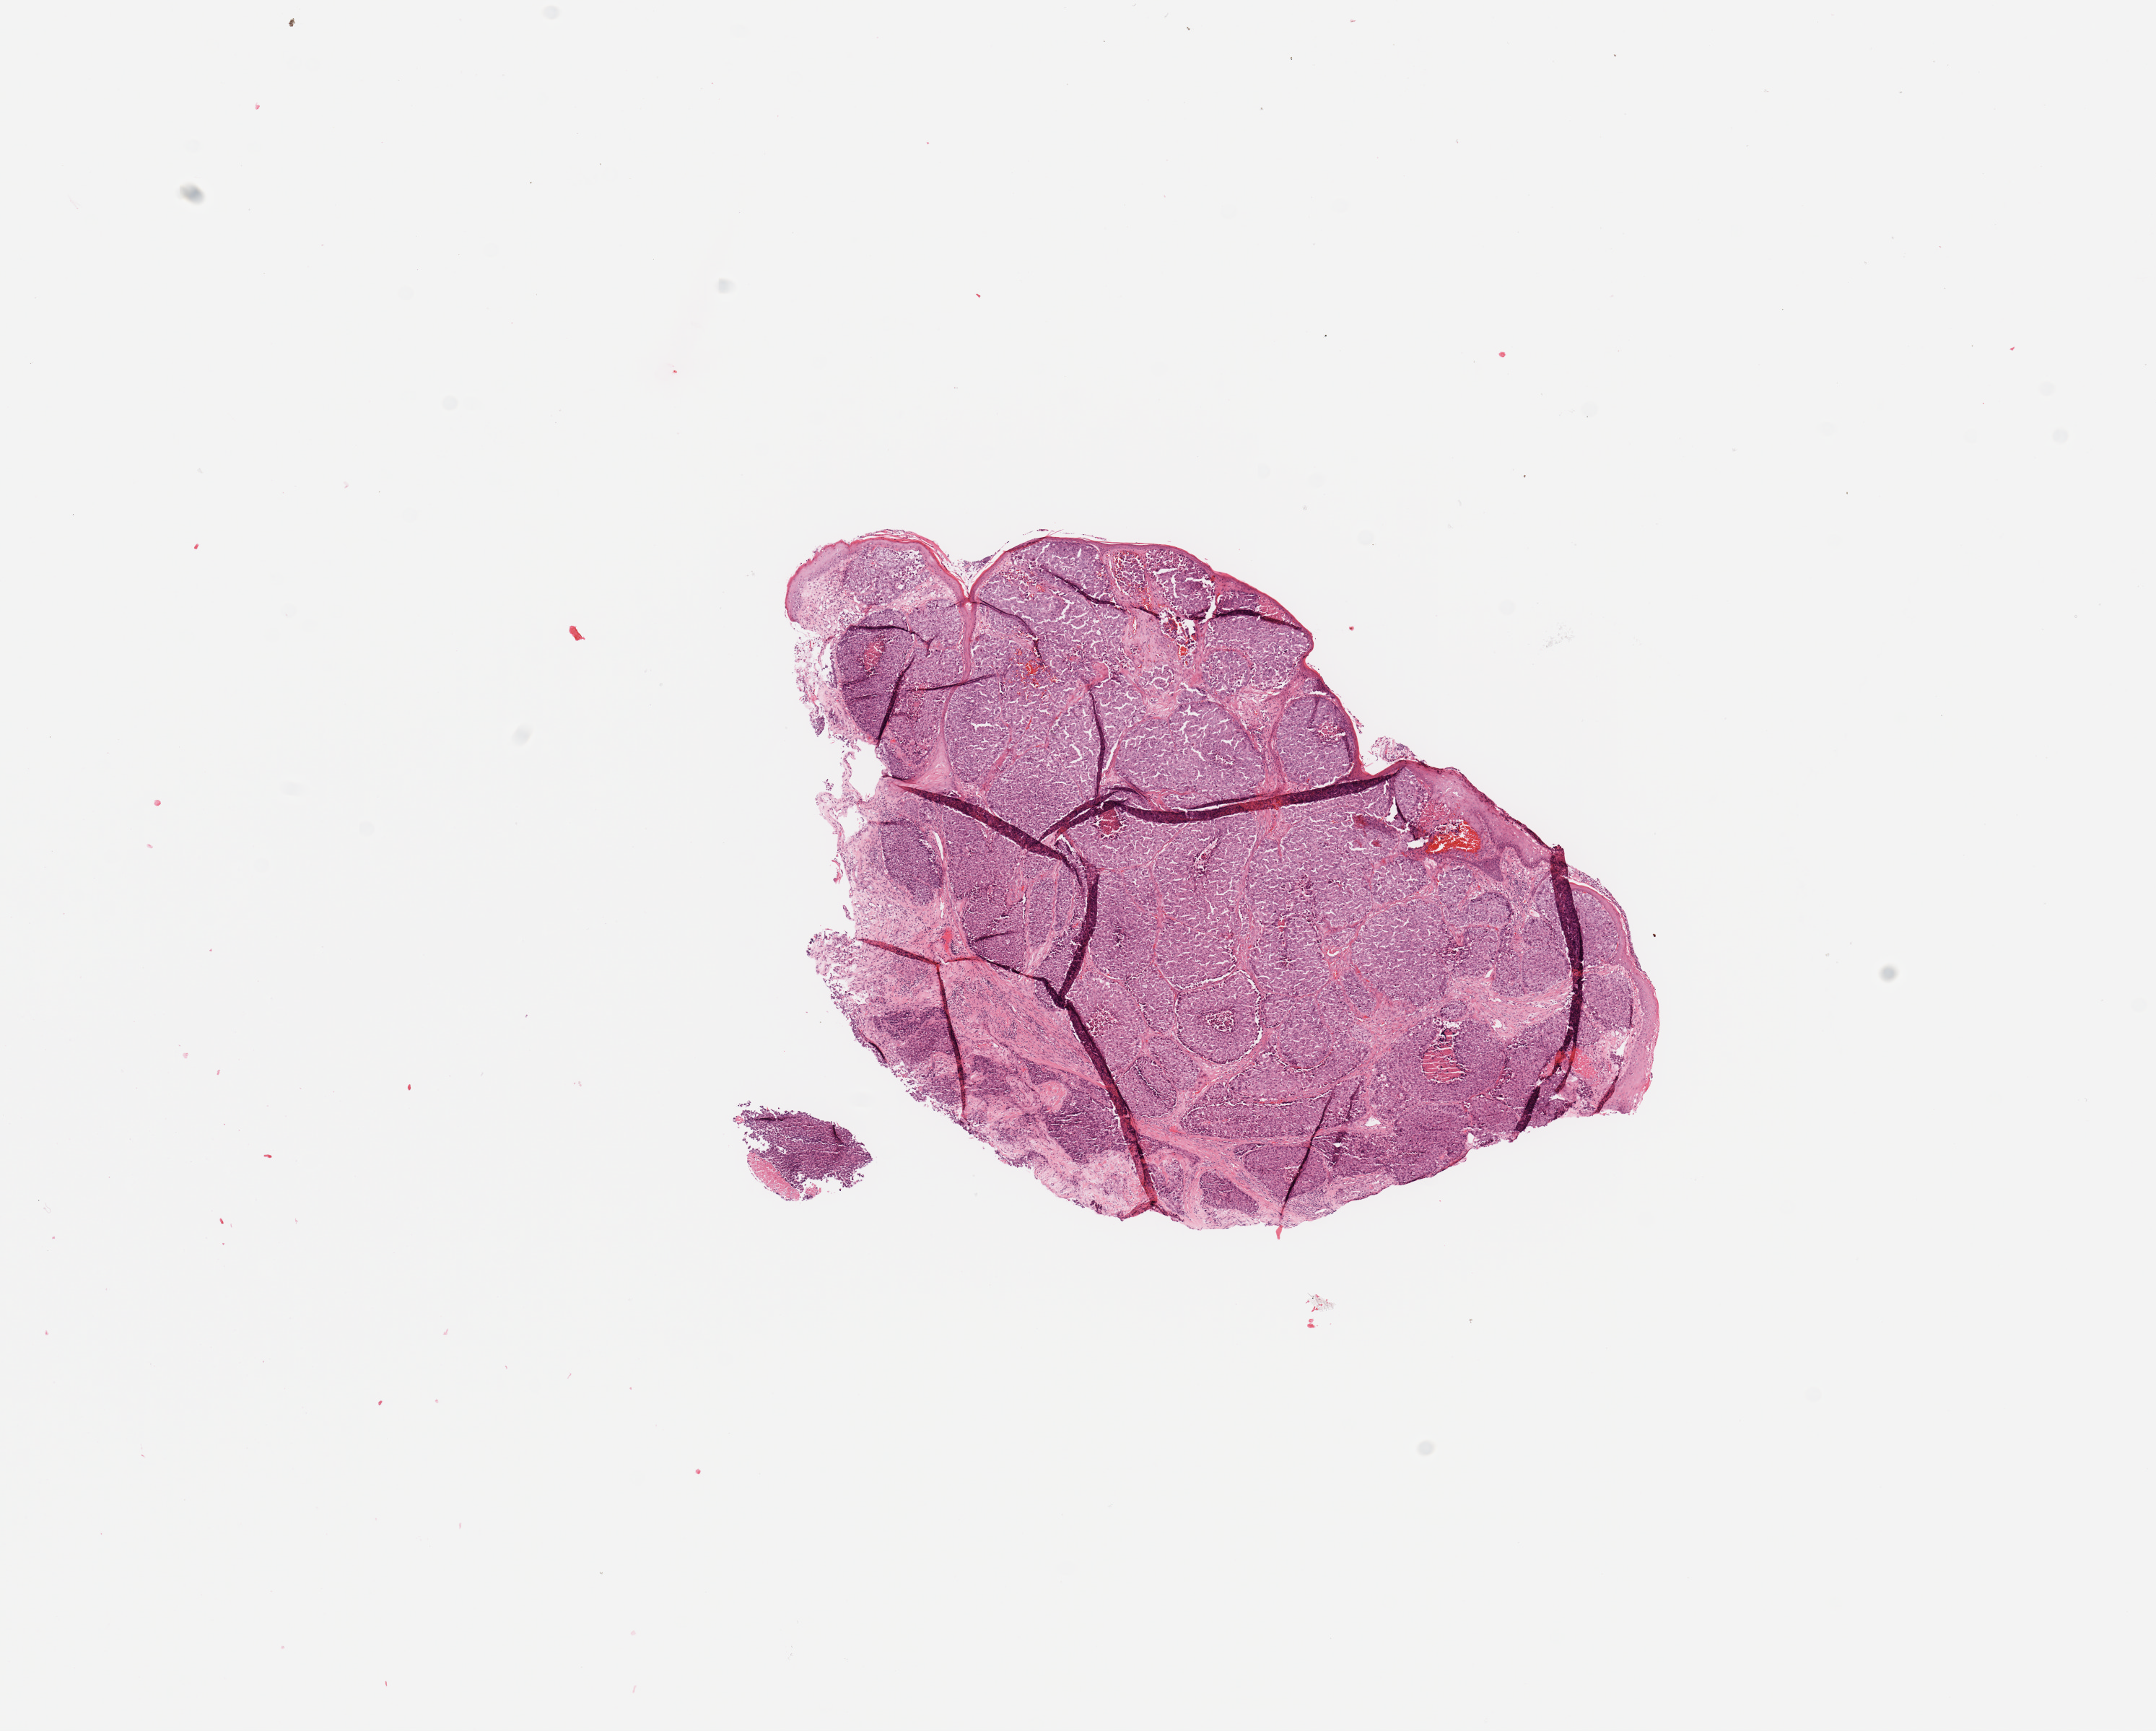
Whole-slide histology image, H&E — whole scanned area (about 11.8 x 9.5 mm, acquisition: 20x scan) shown as a low-resolution overview, tumour tissue sample, sampled site: larynx. 63-year-old female patient. Histologic grade: G3 (poorly differentiated). Pathologist review of this section (percent, as recorded): tumour nuclei 85%, necrosis 15%.
Histologic diagnosis: Squamous cell carcinoma, NOS (larynx, NOS). AJCC pathologic stage: III.